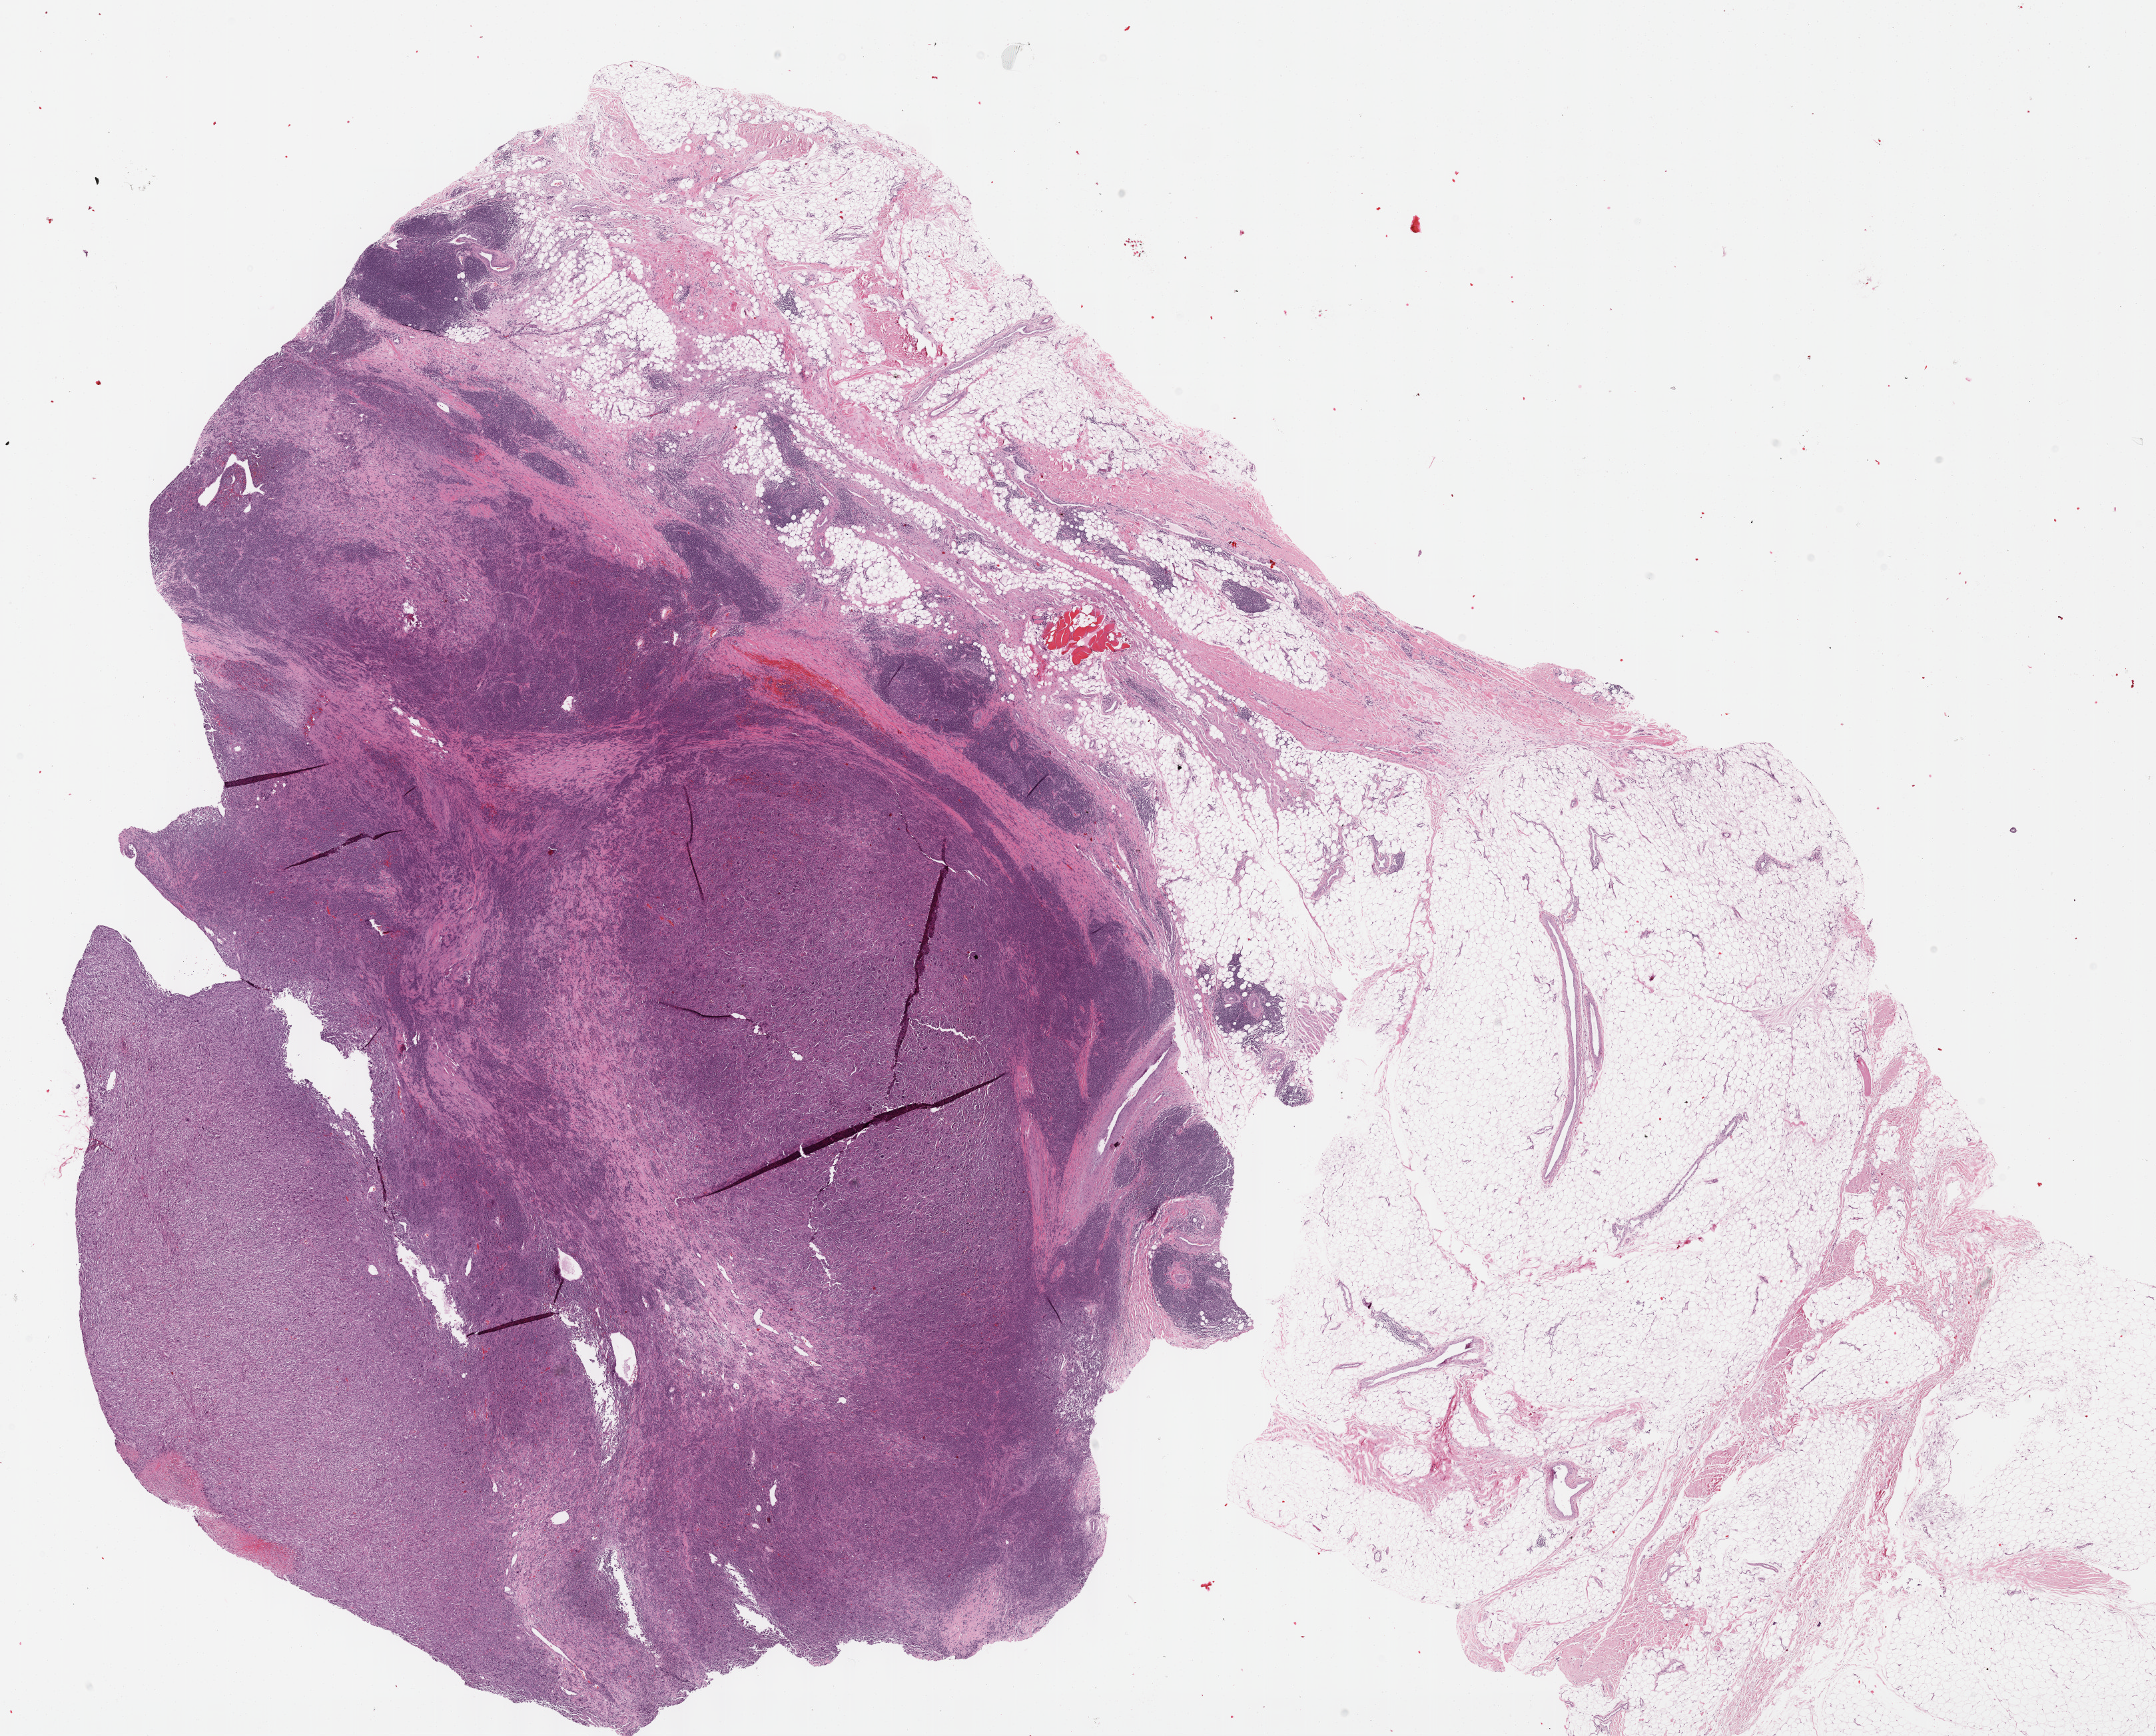
Digitized H&E tissue section (whole slide), shown as a low-resolution overview of the whole scanned area (about 26.2 x 21.1 mm); FFPE section; connective, subcutaneous and other soft tissues, primary tumour sample. Patient: male, age at initial diagnosis 59 years.
Histologic diagnosis: Undifferentiated sarcoma (connective, subcutaneous and other soft tissues of upper limb and shoulder).